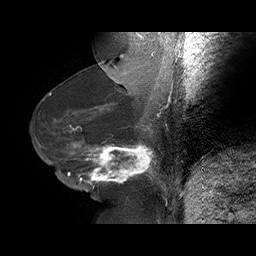
Breast MRI (dynamic contrast-enhanced), one sagittal slice. Dynamic contrast-enhanced series, time point 2 of 6 at this slice position (early post-contrast). 1.5 T. TE 4.5 ms, TR 32.4 ms. 3 mm slice thickness. 256 × 256 image matrix, field of view 180 × 180 mm. Female patient. From the clinical record (not read from this slice): setting: breast cancer imaged before/during neoadjuvant chemotherapy; receptor status: HR-positive, HER2-negative.
Structures marked on this image (semi-automatic segmentation, software-assisted and operator-edited):
- analysis volume of interest (the breast-tissue region the enhancement analysis was run in; not a lesion): bounding box <58,134,166,191> (left, top, right, bottom; pixels)
- tumour enhancement mask (voxels above the 100 % enhancement threshold inside the analysis volume of interest): <67,142,156,184>